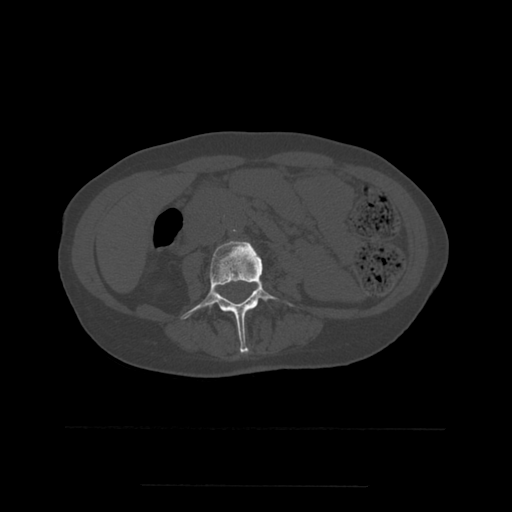
CT including the spine, one axial slice; slice 188 of 544 in the series (ordered by position); bone window (W 1800 / L 400 HU); 1.25 mm slice thickness; 512 × 512 image matrix. Patient age 58 years. Case-level facts recorded for this patient, not image findings: primary cancer: lung.
Structures marked on this image (semi-automatic segmentation, software-assisted and operator-edited):
- L3 vertebra: bounding box [x1, y1, x2, y2] px = [181, 241, 293, 354]